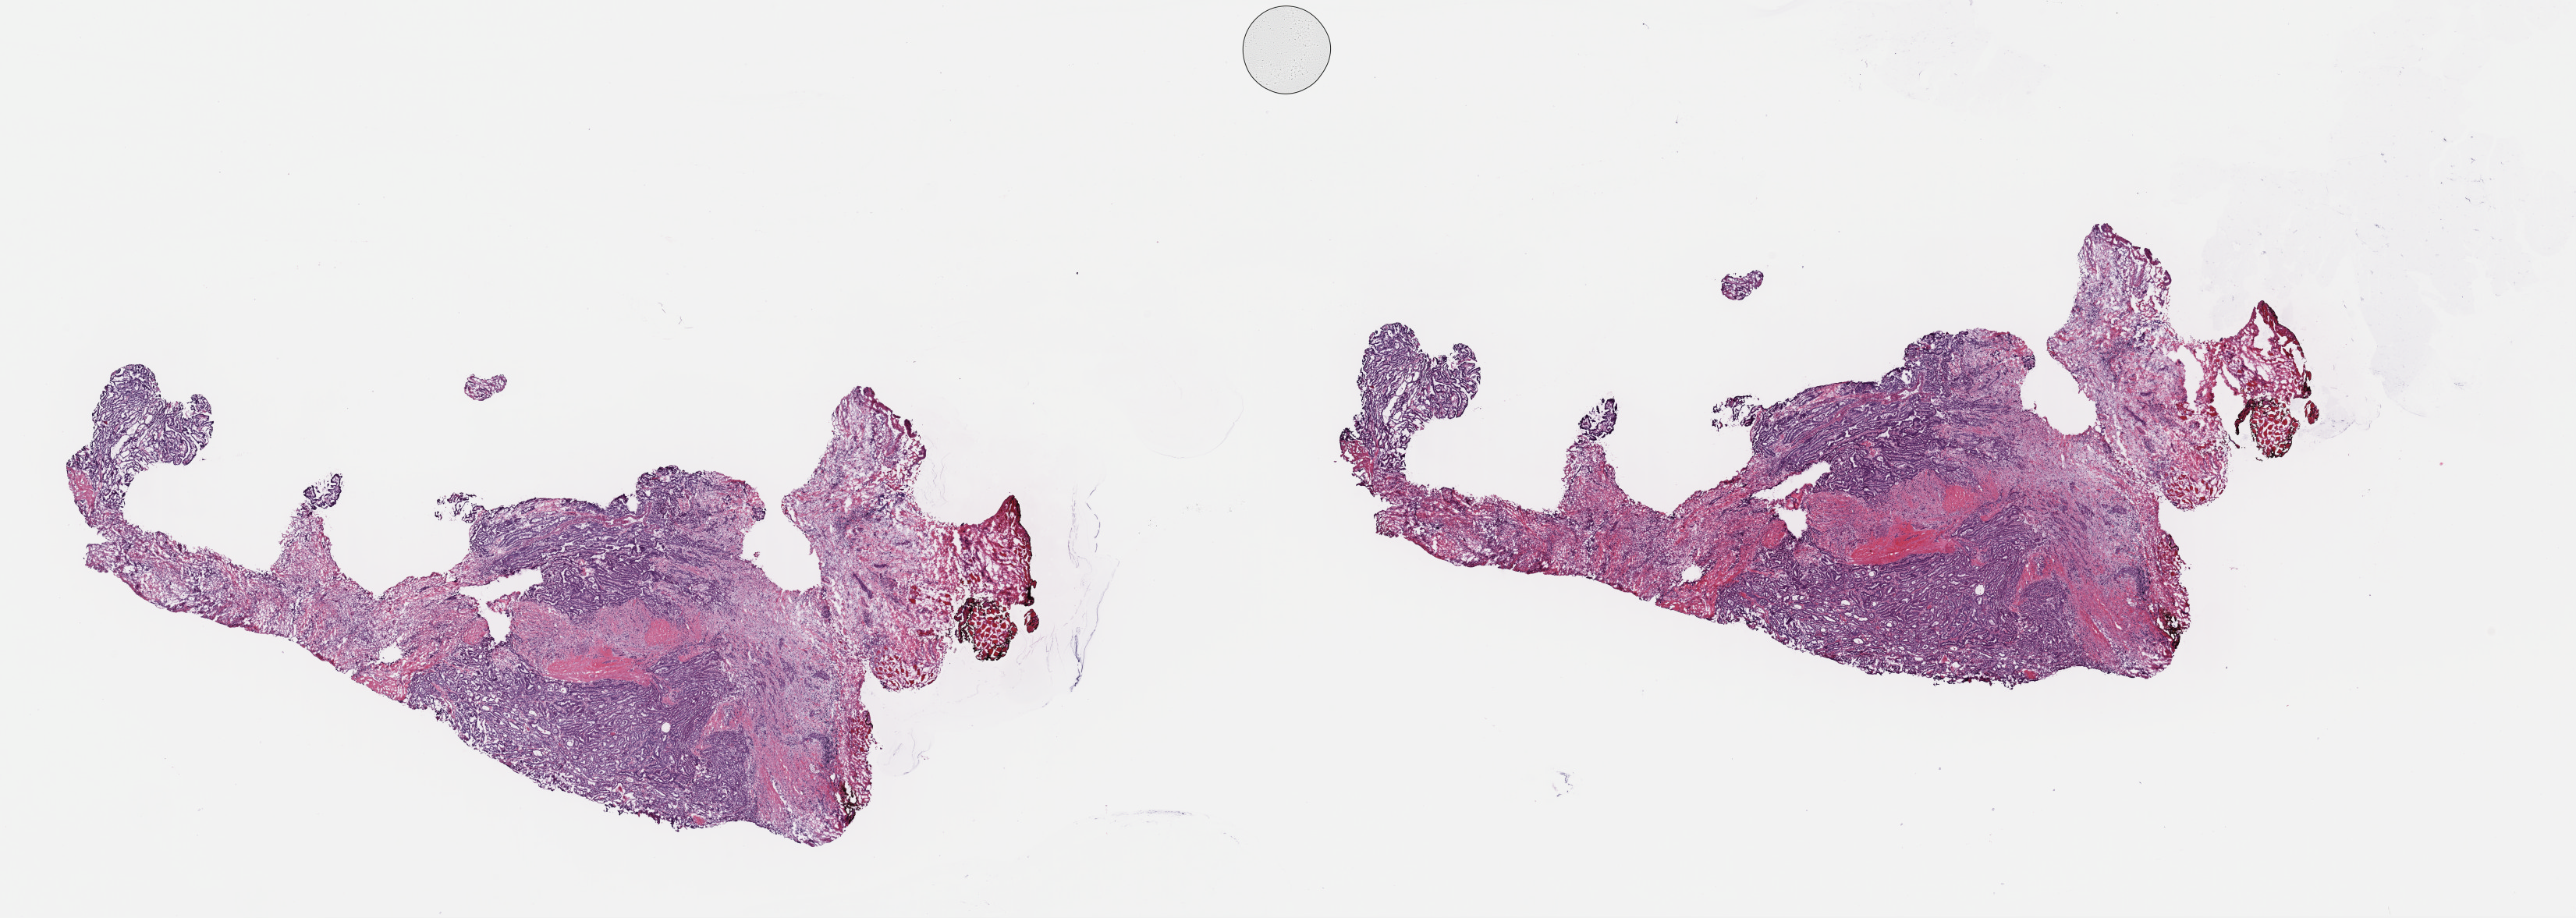
Whole-slide histology image, H&E-stained — low-resolution overview of the scanned area, about 26.1 x 9.3 mm (slide scanned at 40x). Frozen section. Thyroid, primary tumour sample. Female, age 33 years at initial diagnosis. Pathologist review of this section (percent, as recorded): tumour cells 70%, tumour nuclei 80%, normal cells 0%, stromal cells 30%, necrosis 0%. Infiltration values recorded for this section: lymphocyte infiltration 15%, monocyte infiltration 0%, neutrophil infiltration 0%.
- lymph nodes positive (case pathology): 14 of 23 examined
- AJCC pathologic stage: I
- pathologic diagnosis: Papillary adenocarcinoma, NOS (thyroid gland)